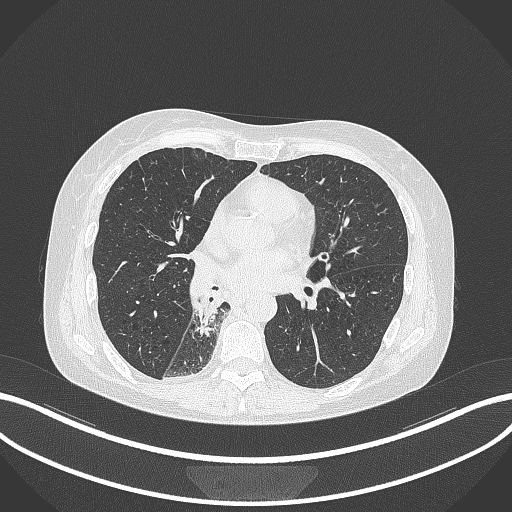
Chest CT, one axial slice; slice 146 of 329 in the series (ordered by position); lung window (W 1500 / L -600 HU); 512 × 512 image matrix, field of view 400 × 400 mm. Female patient, age 63 years. Case-level facts recorded for this patient, not image findings: clinical TNM (as recorded): T1c N0 M0.
Outlined on this slice (bounding box drawn by a radiologist):
- lung tumour (recorded histology: adenocarcinoma): bounding box (x1, y1, x2, y2) in pixels: (191, 286, 222, 336)